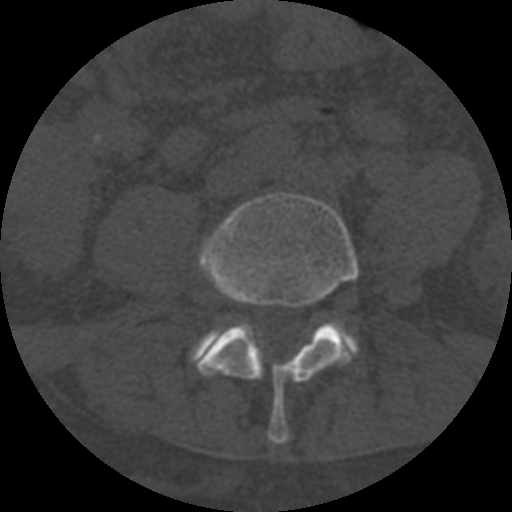
CT including the spine, one axial slice. Slice 202 of 708 in the series (ordered by position). Reconstruction kernel STANDARD. 120 kVp. One of 3 acquisitions stored at this slice position. Bone window (W 1800 / L 400 HU). 1.25 mm slice thickness. 512 × 512 image matrix, field of view 160 × 160 mm. Patient age 55 years. From the clinical record (not read from this slice): primary cancer: colon.
Structures marked on this image (semi-automatic segmentation, software-assisted and operator-edited):
- L4 vertebra: bounding box (x1, y1, x2, y2) in pixels: (197, 193, 359, 445)
- L5 vertebra: (193, 320, 358, 360)